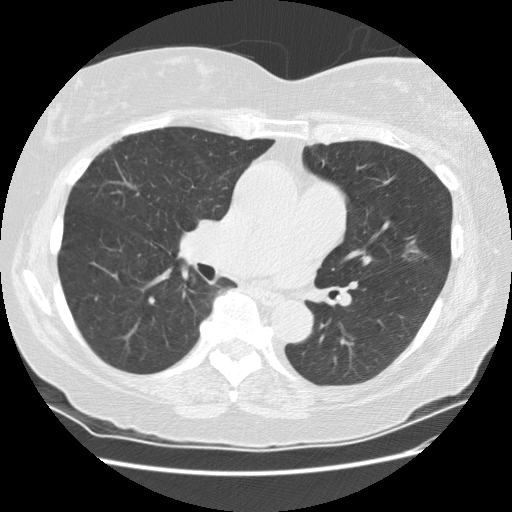
Low-dose screening chest CT, one axial slice; slice 99 of 180 in the series (ordered by position); reconstruction kernel STANDARD; lung window (W 1500 / L -600 HU); 2.5 mm slice thickness; 512 × 512 image matrix.
Outlined on this slice (manually delineated by an expert):
- lesion 1 (tumor, upper lobe of left lung): box from (x=401, y=245) to (x=421, y=261) px